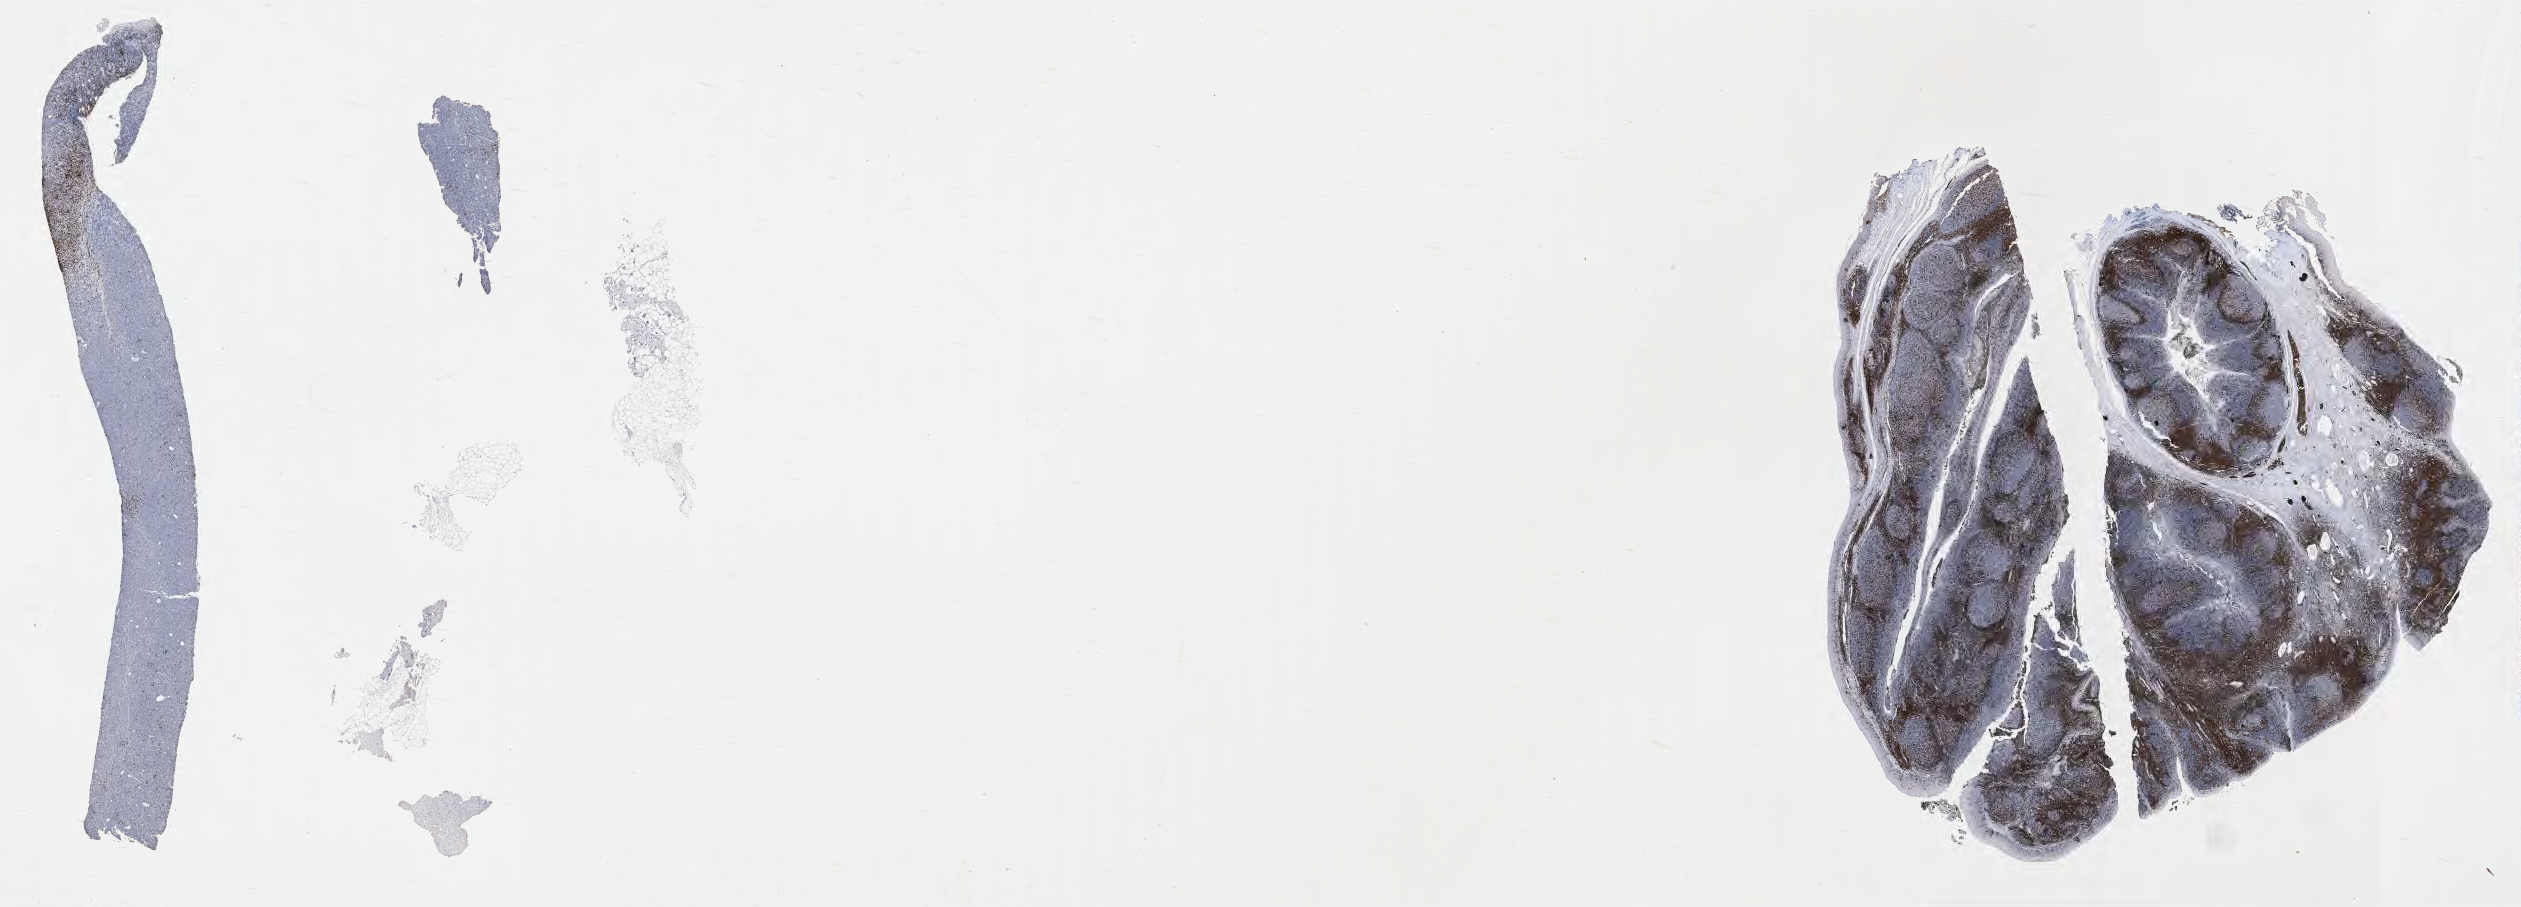
Whole-slide image, immunohistochemical stain for CD3, whole scanned area (about 40.8 x 14.7 mm) shown as a low-resolution overview. Specimen: tumor tissue. Female patient, 61 years old.
Diagnosis: Burkitt lymphoma, NOS.